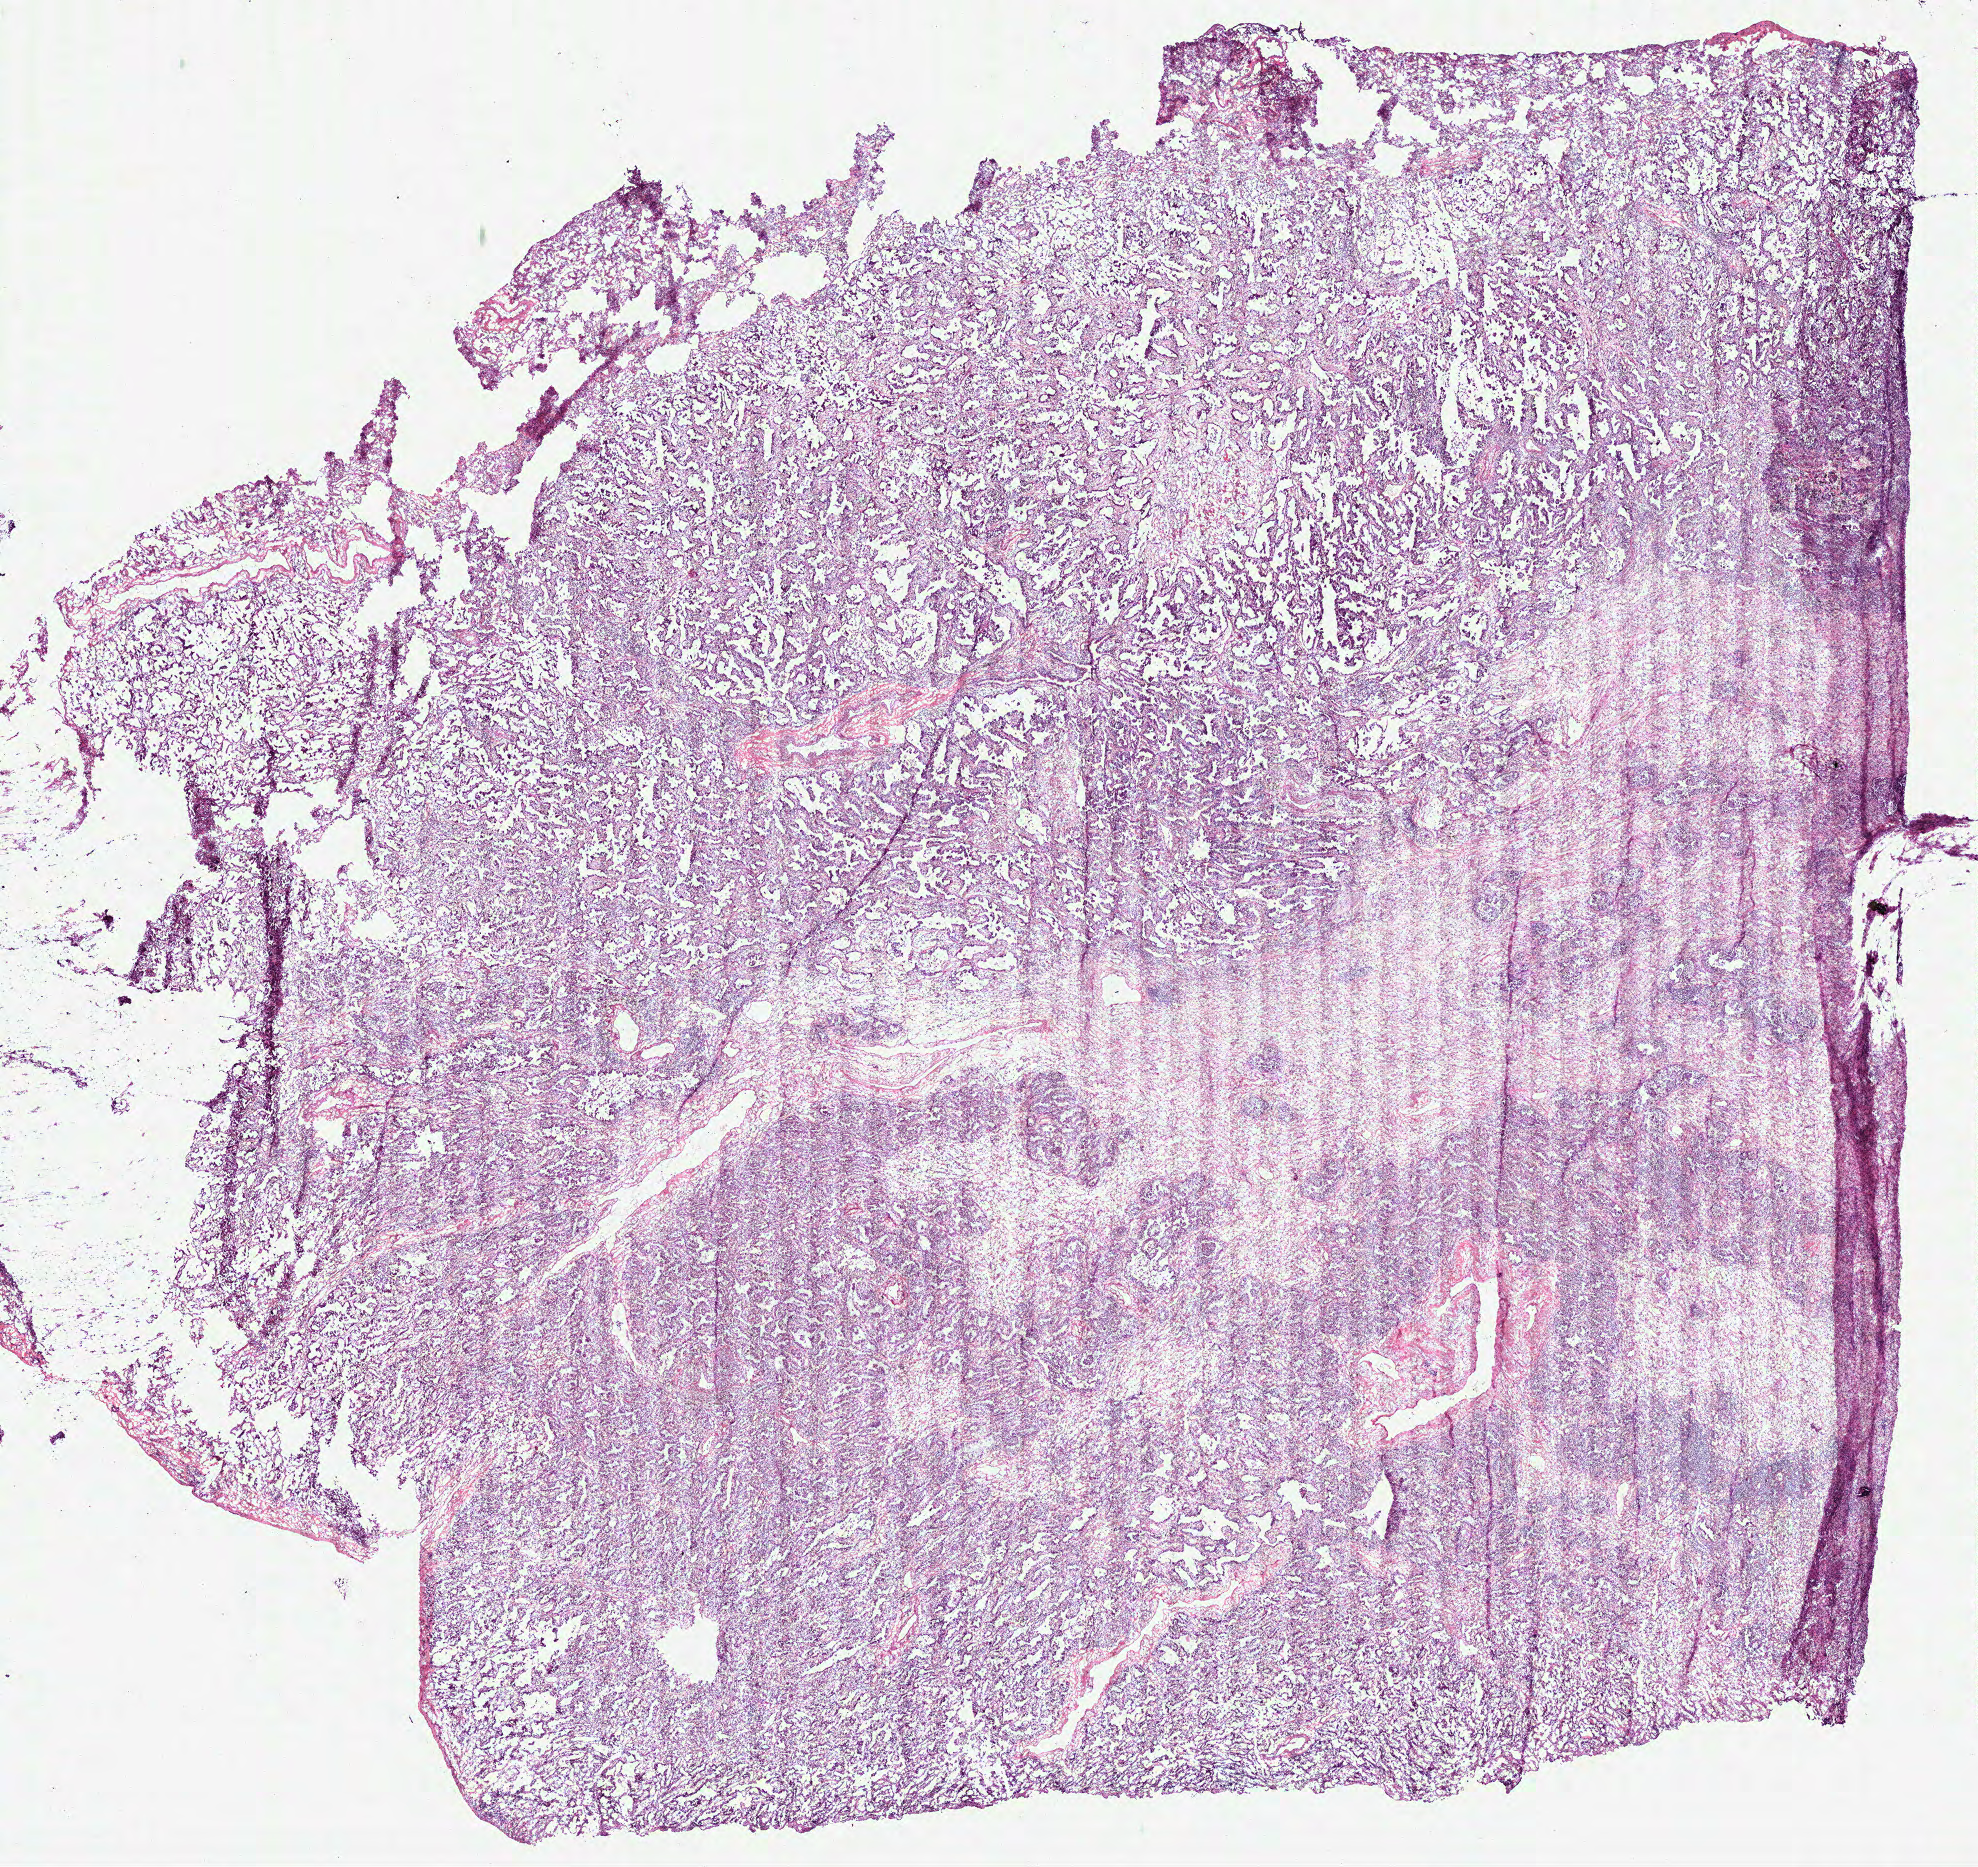
Whole-slide histology image, H&E-stained, whole scanned area (about 16.0 x 15.1 mm, from a 40x scan) shown as a low-resolution overview; frozen section from the bottom of the tissue portion; primary tumour sample from the lung. Female patient; age at initial diagnosis 54 years. Composition of this section per pathologist review: tumour cells 85%, tumour nuclei 75%, normal cells 0%, stromal cells 15%, necrosis 0%.
* AJCC pathologic stage: IIA (7th edition)
* histologic diagnosis: Bronchiolo-alveolar carcinoma, non-mucinous
* TNM: T2b N0 M0